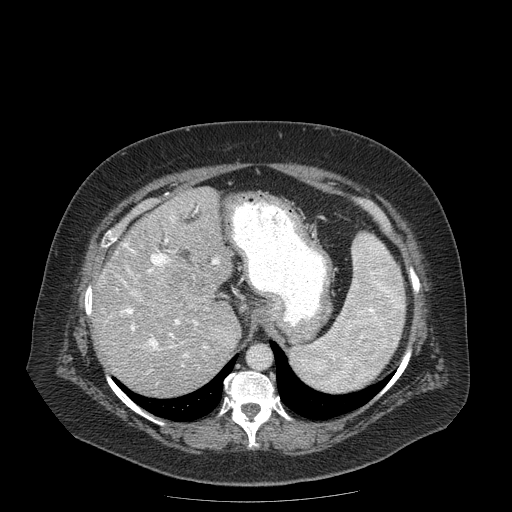
Contrast-enhanced abdominal CT (liver protocol), one axial slice. Position 129 of 204 along the scan axis. Reconstruction kernel STANDARD. 120 kVp. Soft-tissue window (W 400 / L 40 HU). 2.5 mm slice thickness. 512 × 512 image matrix, field of view 440 × 440 mm. Case-level facts recorded for this patient, not image findings: diagnosis: hepatocellular carcinoma (patient treated with transarterial chemoembolisation; whether this scan precedes or follows treatment is not stated here); TNM stage (as recorded): Stage-IIIB; Child-Pugh class: A; tumour differentiation: well differentiated; tumour nodularity: uninodular.
Outlined on this slice (semi-automatically segmented with operator editing):
- abdominal aorta: box from (x=248, y=346) to (x=270, y=368) px
- liver parenchyma outside the tumour (the mass and vessels are separate outlines, so this box may not span the whole liver): (x=94, y=186)–(x=240, y=396)
- mass: (x=148, y=261)–(x=217, y=316)
- liver vessels: (x=120, y=209)–(x=220, y=372)